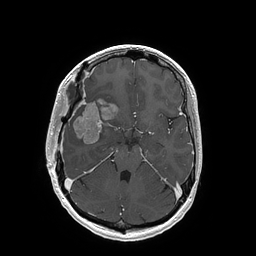
Brain MRI from a brain-tumour surgery series, one axial slice. Slice 108 of 202 in the series (ordered by position). T1-weighted post-contrast. 1 mm slice thickness. 256 × 256 image matrix, field of view 250 × 250 mm. From the clinical record (not read from this slice): histopathology: Glioblastoma; WHO grade: 4; IDH mutation: no; tumour location: Right Insular.
Outlined on this slice (outlined manually by an expert reader):
- tumour: box from (x=73, y=100) to (x=118, y=144) px